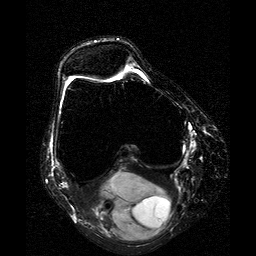
MRI of an extremity soft-tissue mass, one axial slice; position 10 of 25 along the scan axis; T2-weighted fat-saturated; 256 × 256 image matrix. Female patient. From the clinical record (not read from this slice): histological type: liposarcoma; site of the primary tumour: right thigh.
Structures marked on this image (expert manual segmentation):
- gross tumour volume (mass): bounding box <91,172,172,242> (left, top, right, bottom; pixels)